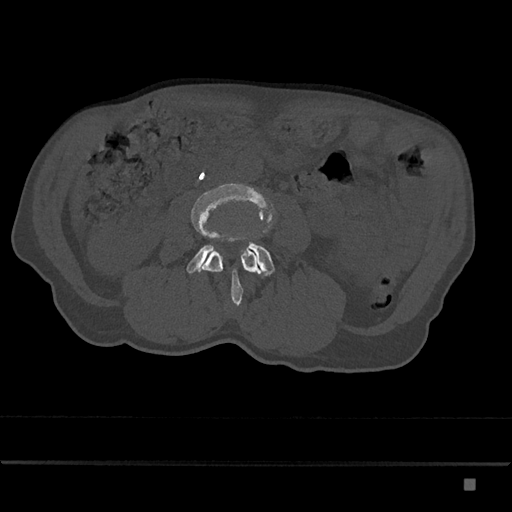
CT including the spine, one axial slice; position 376 of 797 along the scan axis; reconstruction kernel Br40s/3; bone window (W 1800 / L 400 HU); 0.5 mm slice thickness; 512 × 512 image matrix, field of view 390 × 390 mm. Patient: male, 72 years. From the clinical record (not read from this slice): primary cancer: prostate.
Annotated regions visible in this slice (semi-automatic segmentation, software-assisted and operator-edited):
- L3 vertebra: box from (x=191, y=183) to (x=272, y=306) px
- L4 vertebra: (x=187, y=242)–(x=275, y=278)